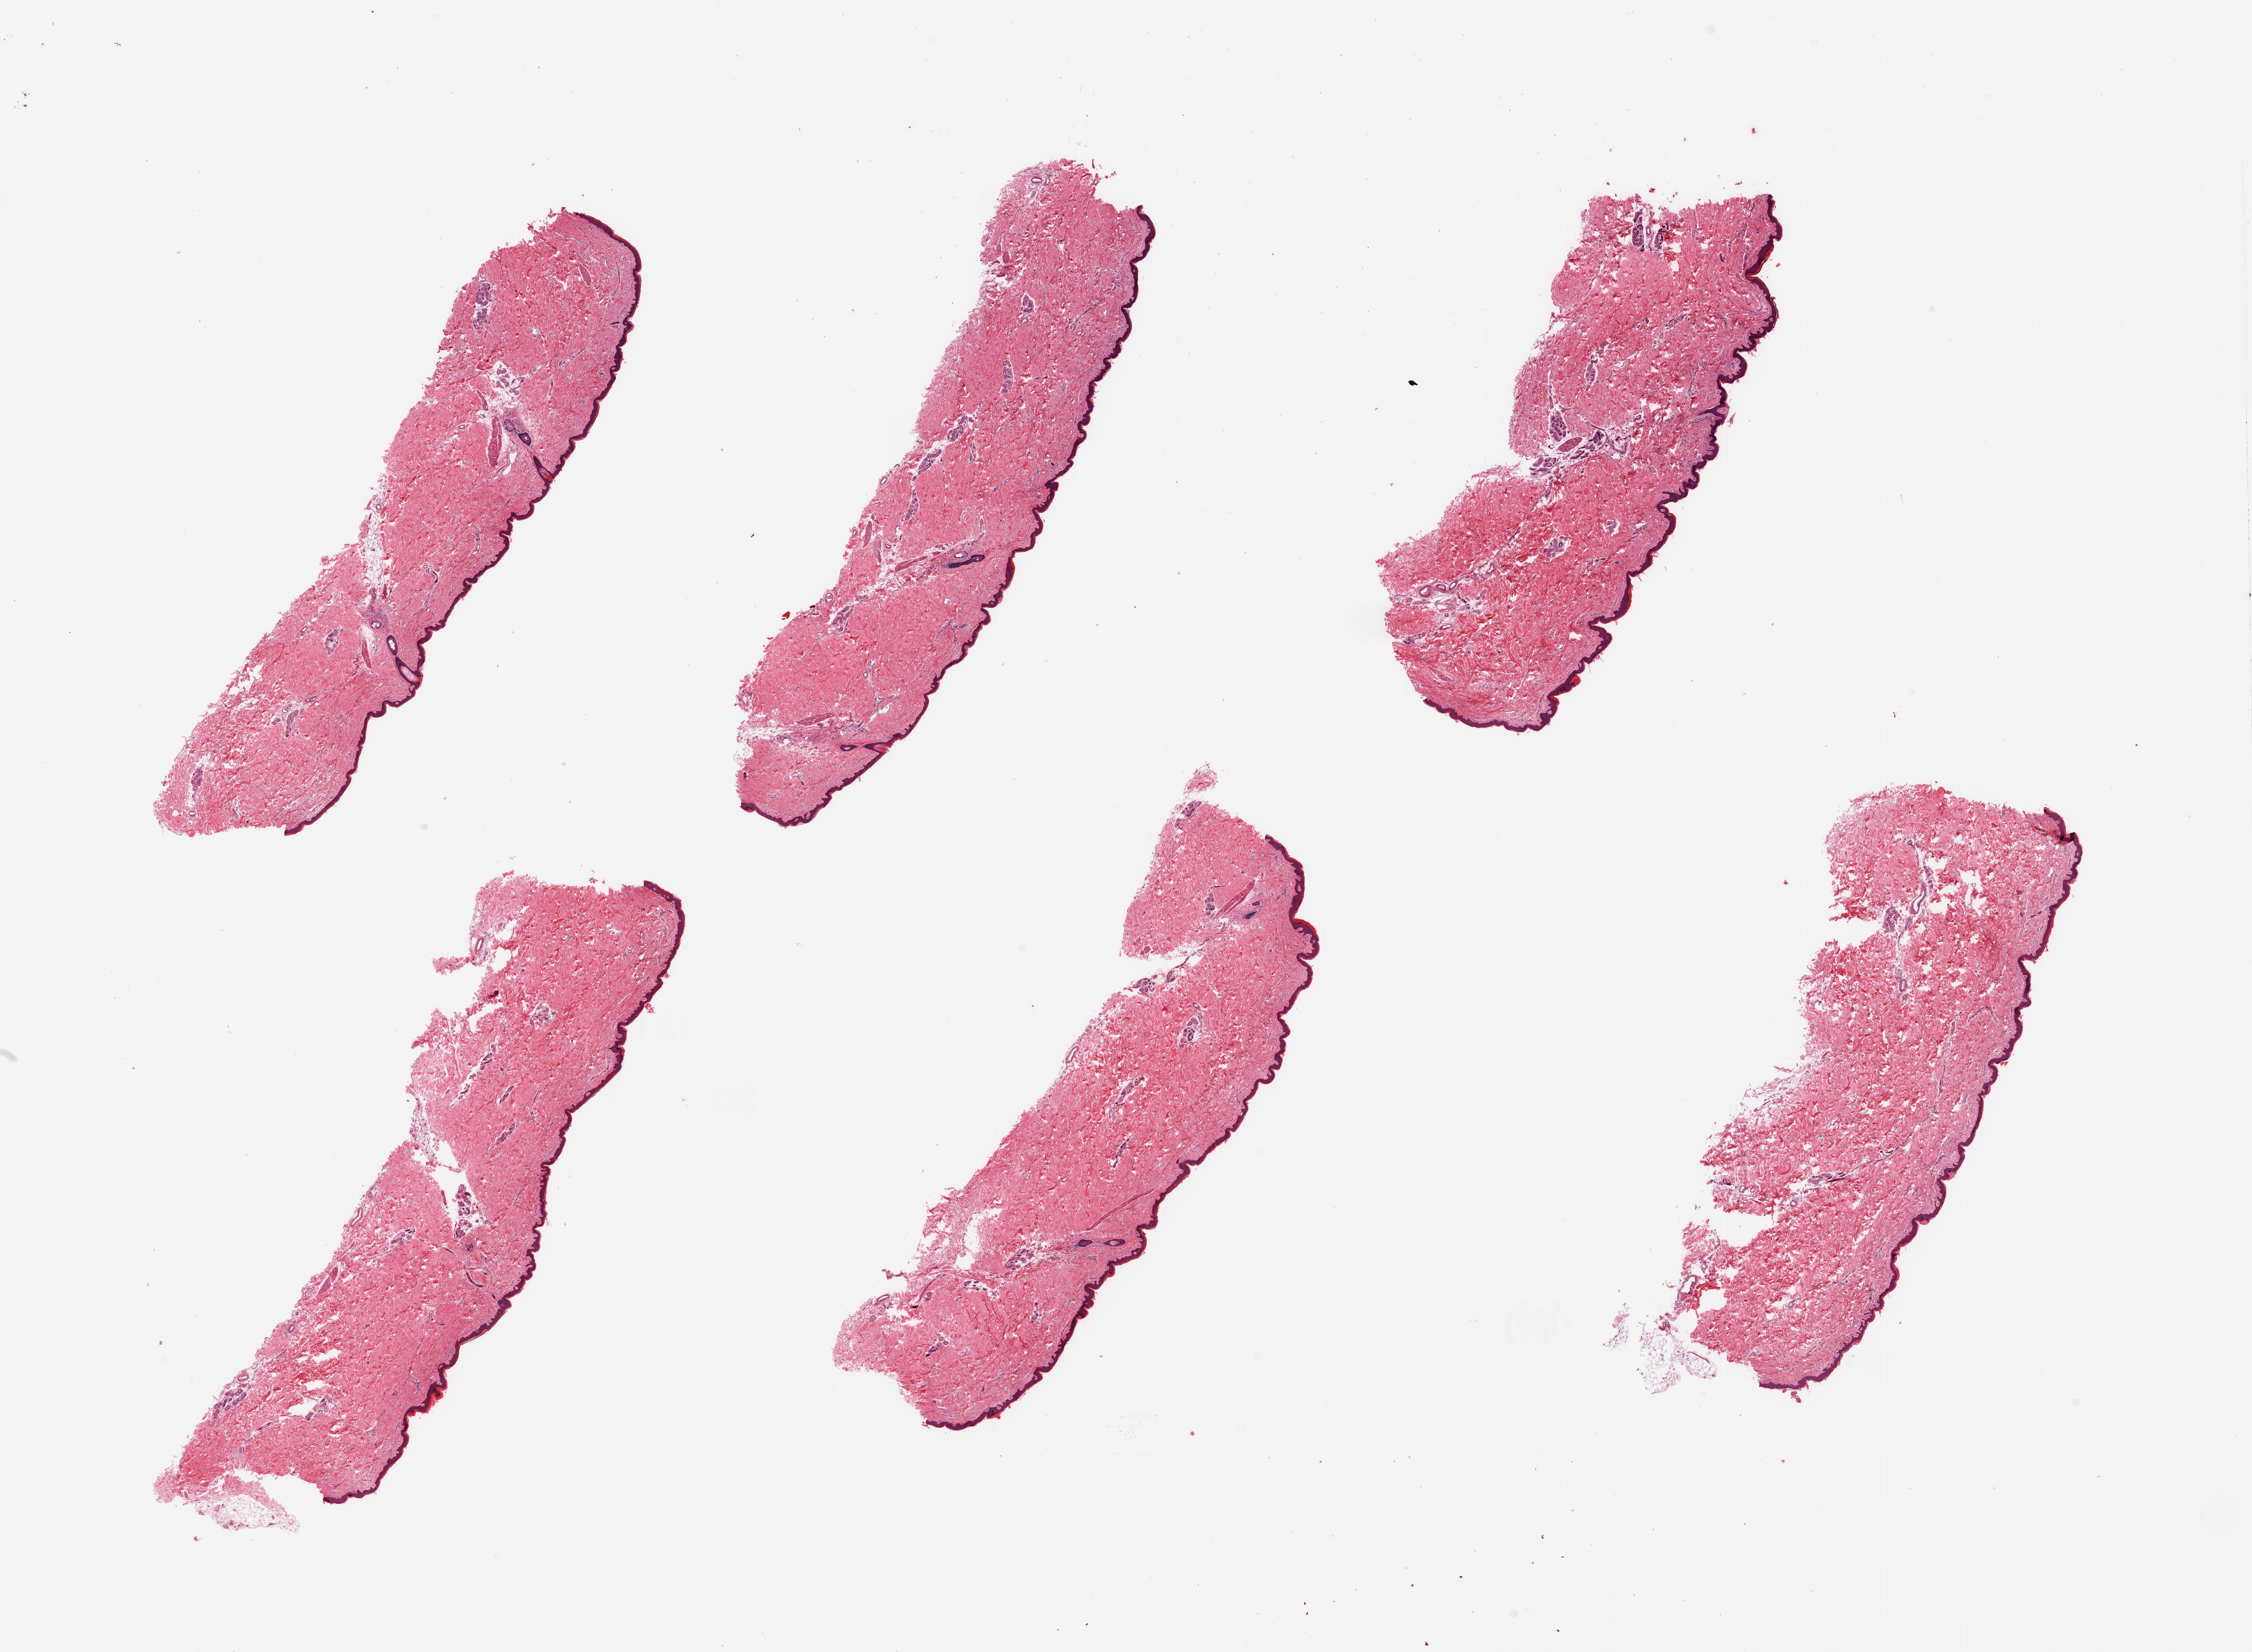
Digitized H&E-stained section, brightfield — low-resolution overview of the scanned area, about 27.6 x 20.2 mm (from a 20x scan). PAXgene-fixed, paraffin-embedded tissue. Section of skin of lower leg (target tissue). Tissue donor sample. Donor sex: female.
Review note (as recorded): 6 pieces; well trimmed; 1% dermal fat.